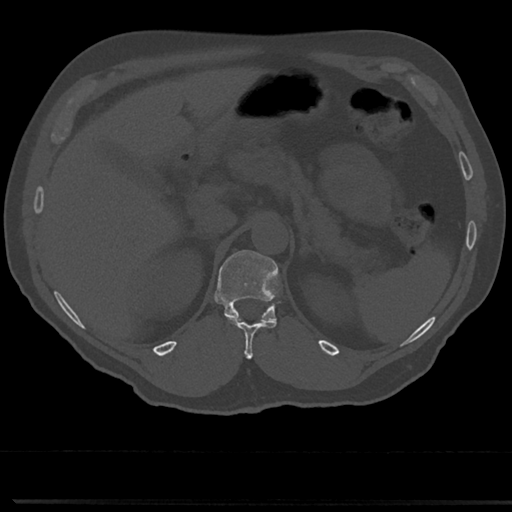
CT including the spine, one axial slice; reconstruction kernel Br40s/3; bone window (W 1800 / L 400 HU); 0.5 mm slice thickness; 512 × 512 image matrix, field of view 355 × 355 mm. Male patient, age 61 years. From the clinical record (not read from this slice): primary cancer: prostate.
Annotated regions visible in this slice (semi-automatically segmented with operator editing):
- T11 vertebra: bounding box [x1, y1, x2, y2] px = [242, 322, 273, 358]
- T12 vertebra: [214, 250, 285, 336]